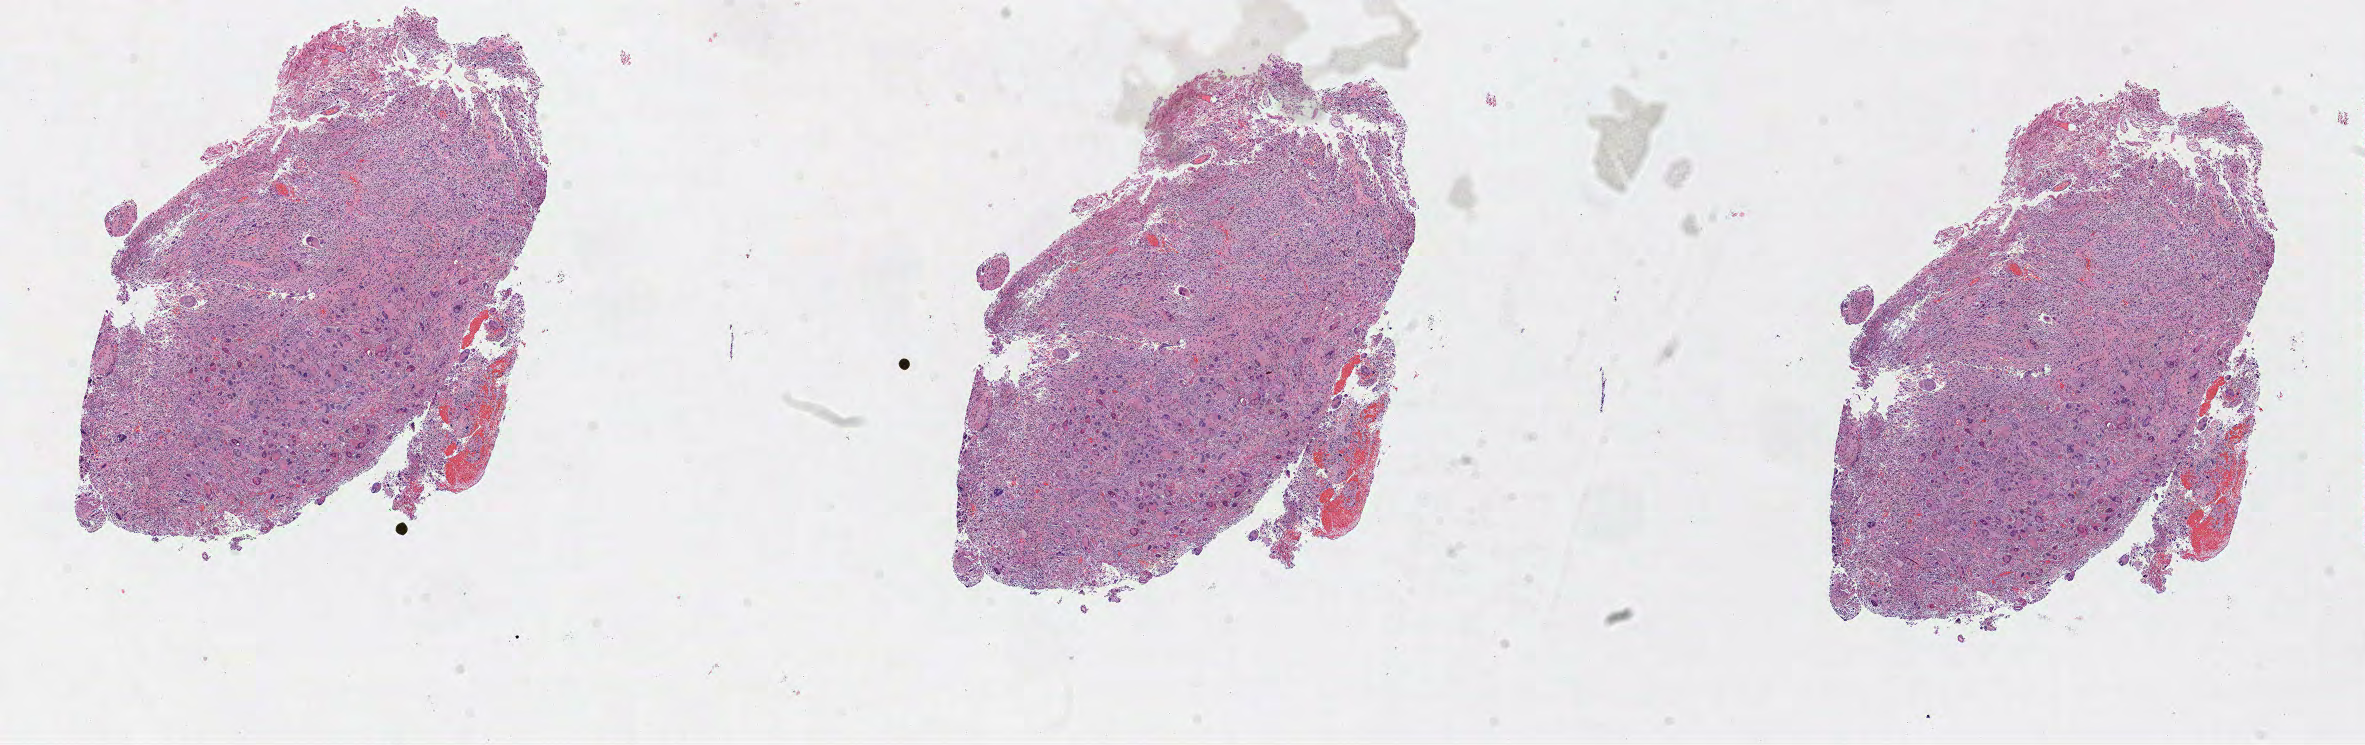
Whole-slide histology image, H&E — whole scanned area (about 19.1 x 6.0 mm, from a 40x scan) shown as a low-resolution overview. Frozen section from the top of the tissue portion. Brain, primary tumour sample. Female patient; age at initial diagnosis 53 years. Slide review estimates, as recorded: tumour cells 100%, tumour nuclei 85%, normal cells 0%, stromal cells 0%, necrosis 0%.
Diagnosis: Glioblastoma.